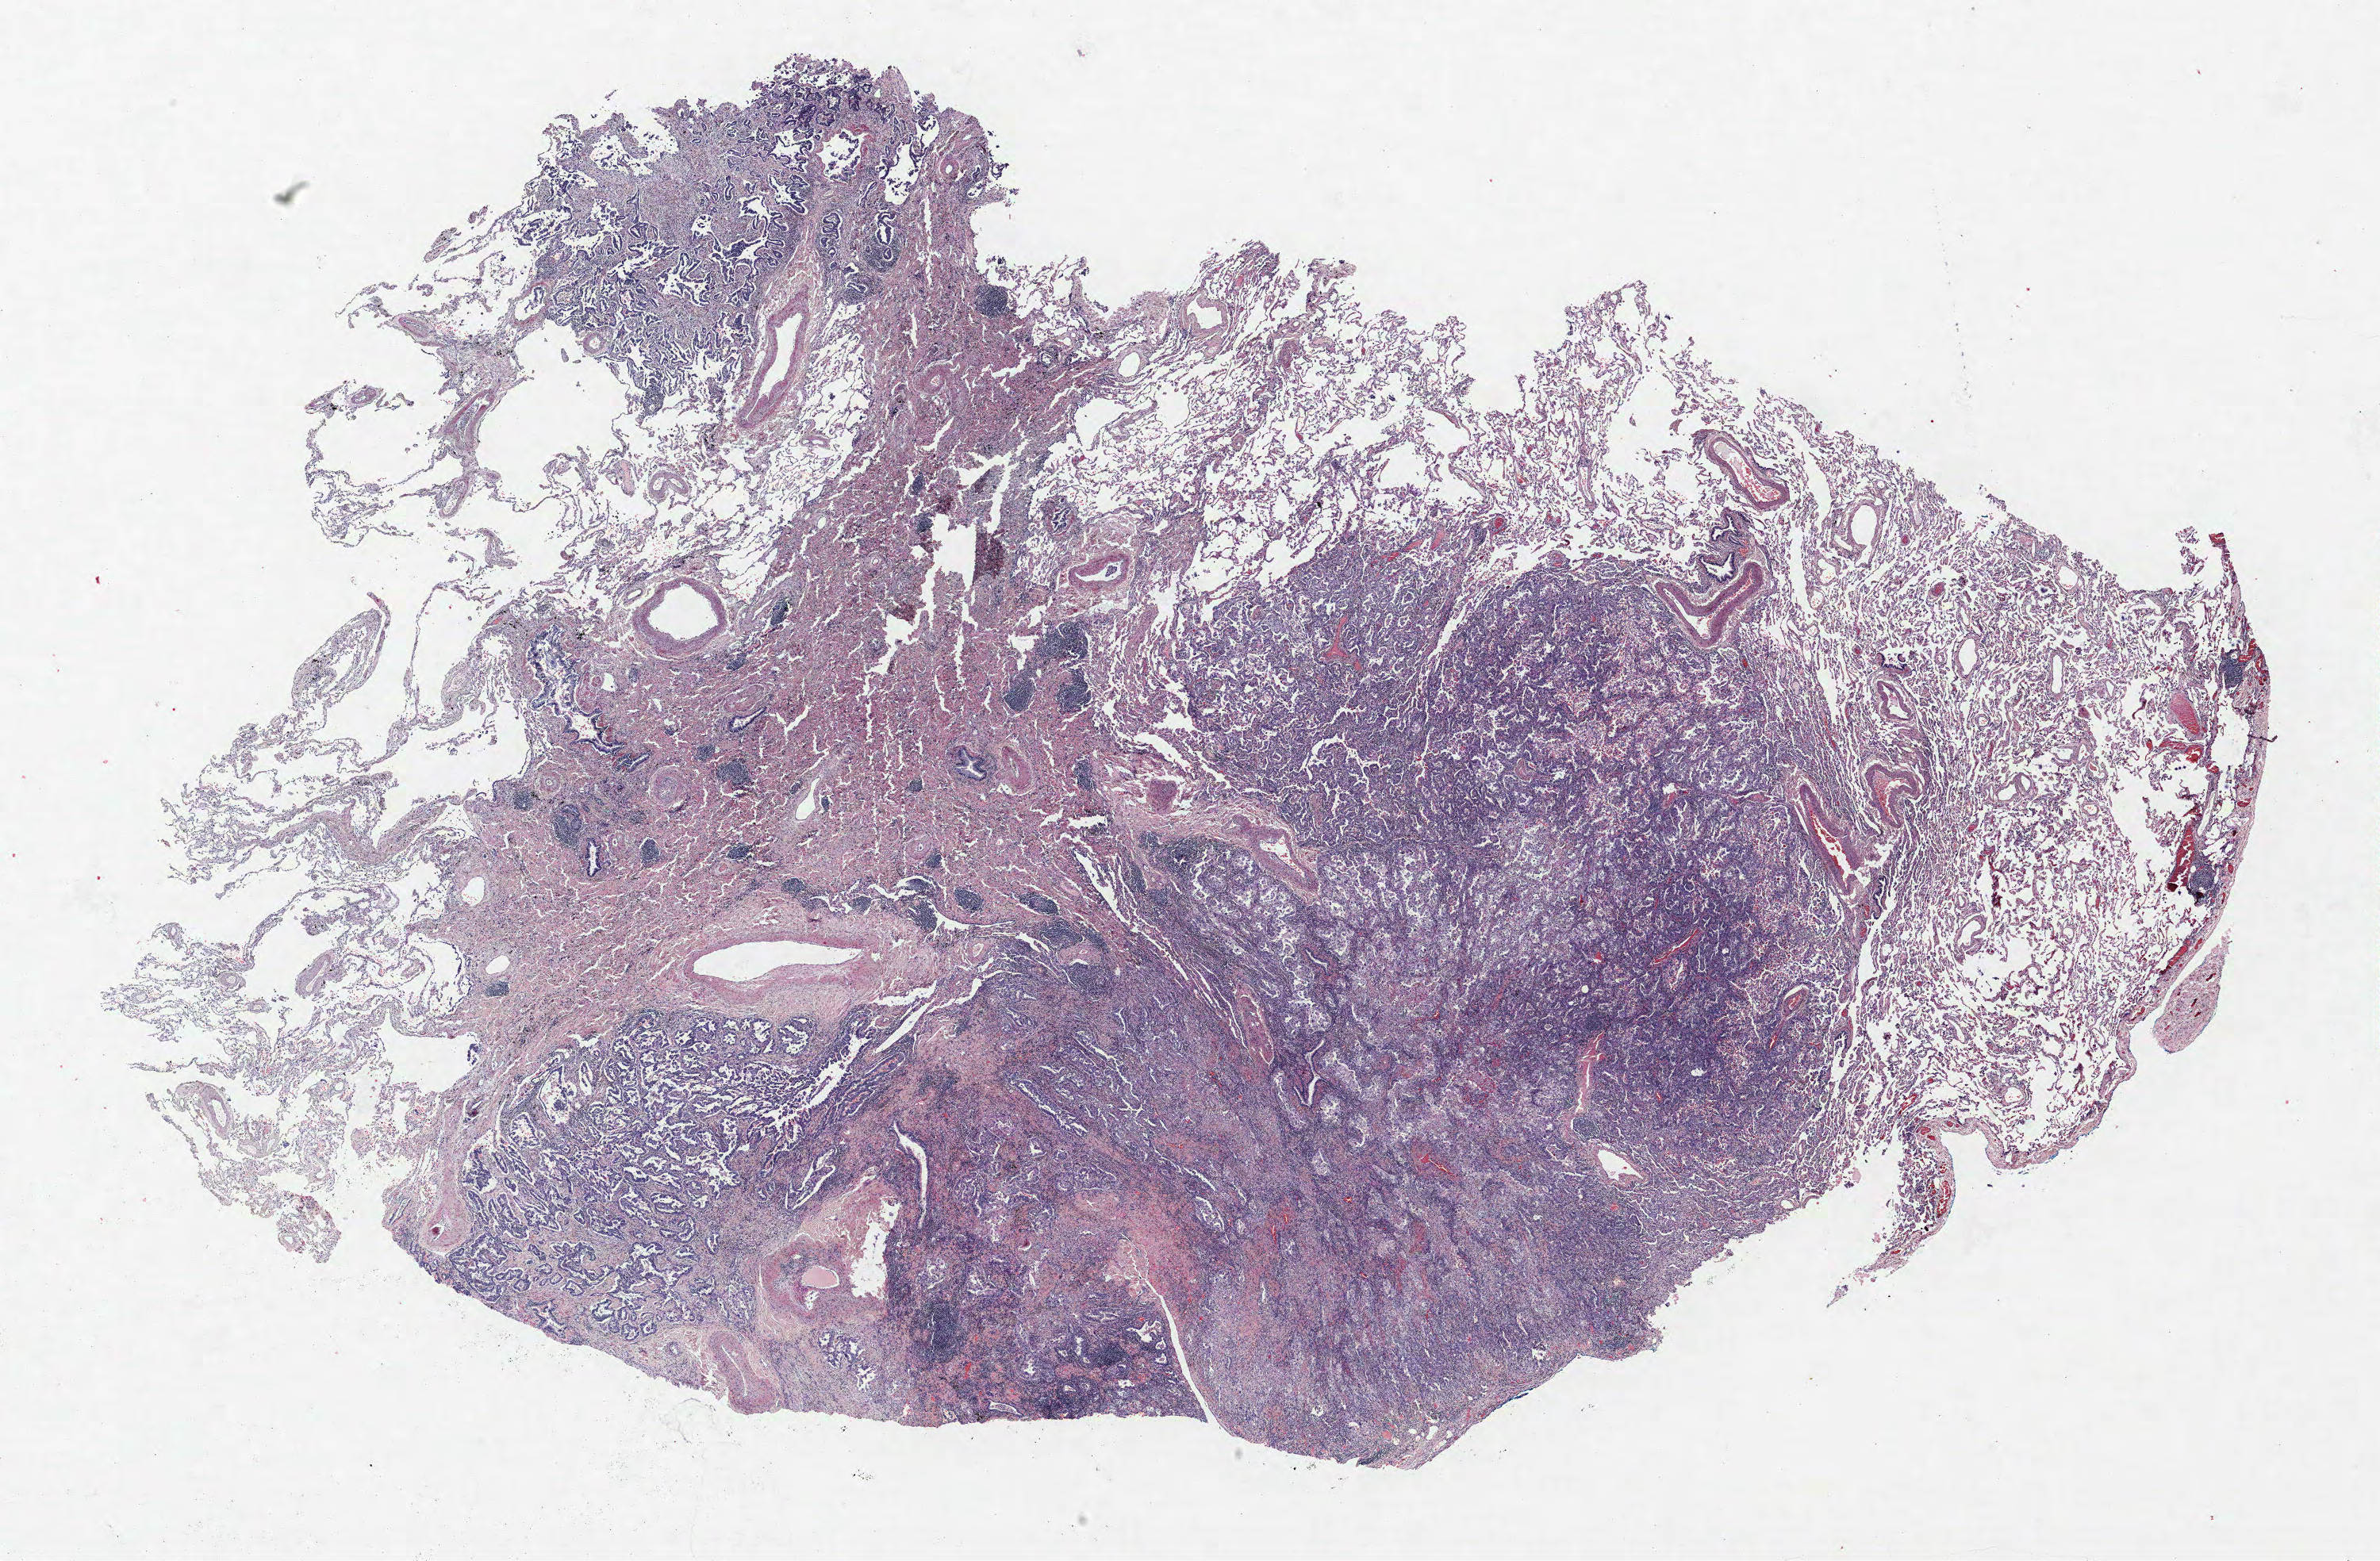
H&E-stained whole-slide image — low-resolution overview of the scanned area, about 24.0 x 15.7 mm (acquisition: 40x scan). FFPE section. Lung. Male, age 70 at enrolment. Current smoker at enrolment.
Participant's lung-cancer diagnosis: Adenocarcinoma, NOS.